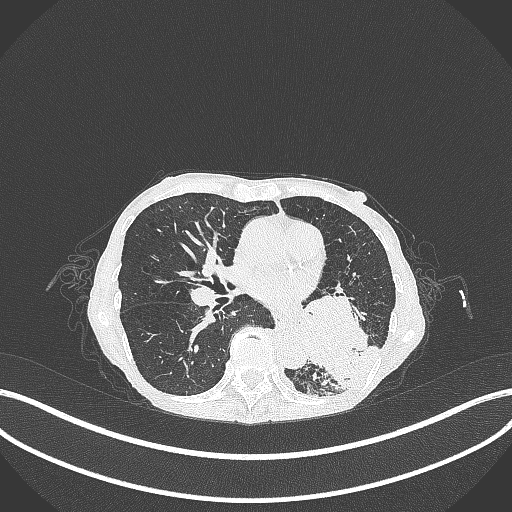
Chest CT, one axial slice. Slice 132 of 347 in the series (ordered by position). Reconstruction kernel B70f. Lung window (W 1500 / L -600 HU). 1 mm slice thickness. 512 × 512 image matrix, field of view 400 × 400 mm. Patient: female, 70 years. Case-level facts recorded for this patient, not image findings: clinical TNM (as recorded): T3 N0 M0.
Annotated regions visible in this slice (rectangle marked by the reading radiologist):
- lung tumour (recorded histology: small cell carcinoma): bounding box [x1, y1, x2, y2] px = [293, 280, 376, 386]